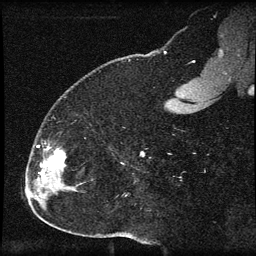
Breast MRI (dynamic contrast-enhanced), one sagittal slice. Position 21 of 60 along the scan axis. Dynamic contrast-enhanced series, image 2 of 3 at this slice position (ordered by acquisition). 1.5 T. TE 4.2 ms, TR 8.2 ms. 2 mm slice thickness. 256 × 256 image matrix, field of view 180 × 180 mm. Patient: female, 32 years.
Outlined on this slice (semi-automatically segmented with operator editing):
- analysis volume of interest (the breast-tissue region the enhancement analysis was run in; not a lesion): bounding box (x1, y1, x2, y2) in pixels: (31, 143, 66, 184)
- tumour enhancement mask (voxels above the 70 % enhancement threshold inside the analysis volume of interest): (37, 145, 66, 181)